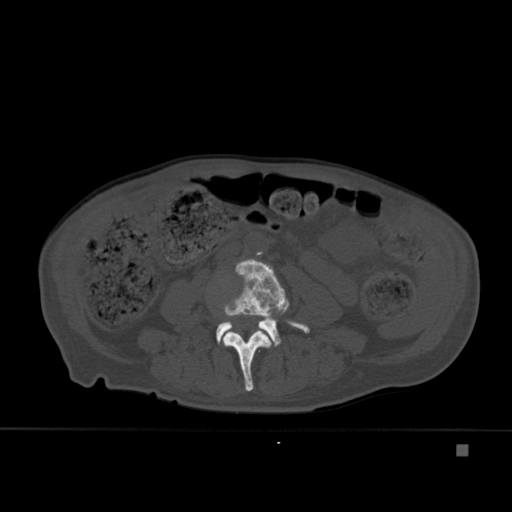
CT including the spine, one axial slice; slice 134 of 451 in the series (ordered by position); bone window (W 1800 / L 400 HU); 512 × 512 image matrix, field of view 378 × 378 mm. Male patient, age 75 years. From the clinical record (not read from this slice): primary cancer: prostate.
Outlined on this slice (semi-automatic segmentation, software-assisted and operator-edited):
- L3 vertebra: bounding box (x1, y1, x2, y2) in pixels: (223, 330, 272, 391)
- L4 vertebra: (216, 259, 310, 347)